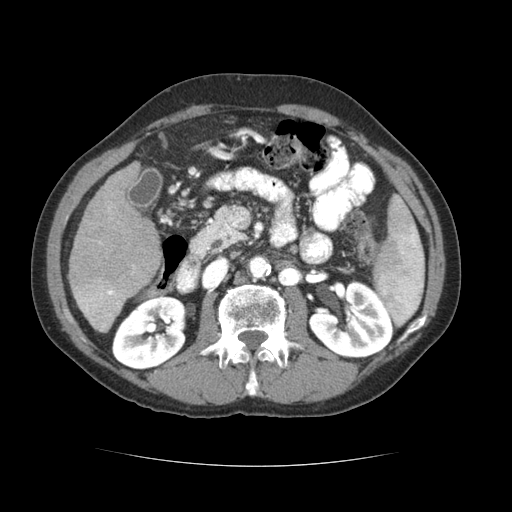
Contrast-enhanced abdominal CT (liver protocol), one axial slice; slice 26 of 69 in the series (ordered by position); soft-tissue window (W 400 / L 40 HU); 2.5 mm slice thickness; 512 × 512 image matrix, field of view 360 × 360 mm. Case-level facts recorded for this patient, not image findings: diagnosis: hepatocellular carcinoma (patient treated with transarterial chemoembolisation; whether this scan precedes or follows treatment is not stated here); TNM stage (as recorded): Stage-II; Child-Pugh class: B; tumour differentiation: poorly differentiated; tumour nodularity: multinodular.
Structures marked on this image (semi-automatically segmented with operator editing):
- liver parenchyma outside the tumour (the mass and vessels are separate outlines, so this box may not span the whole liver): bounding box <68,162,160,332> (left, top, right, bottom; pixels)
- liver vessels: <76,207,135,329>